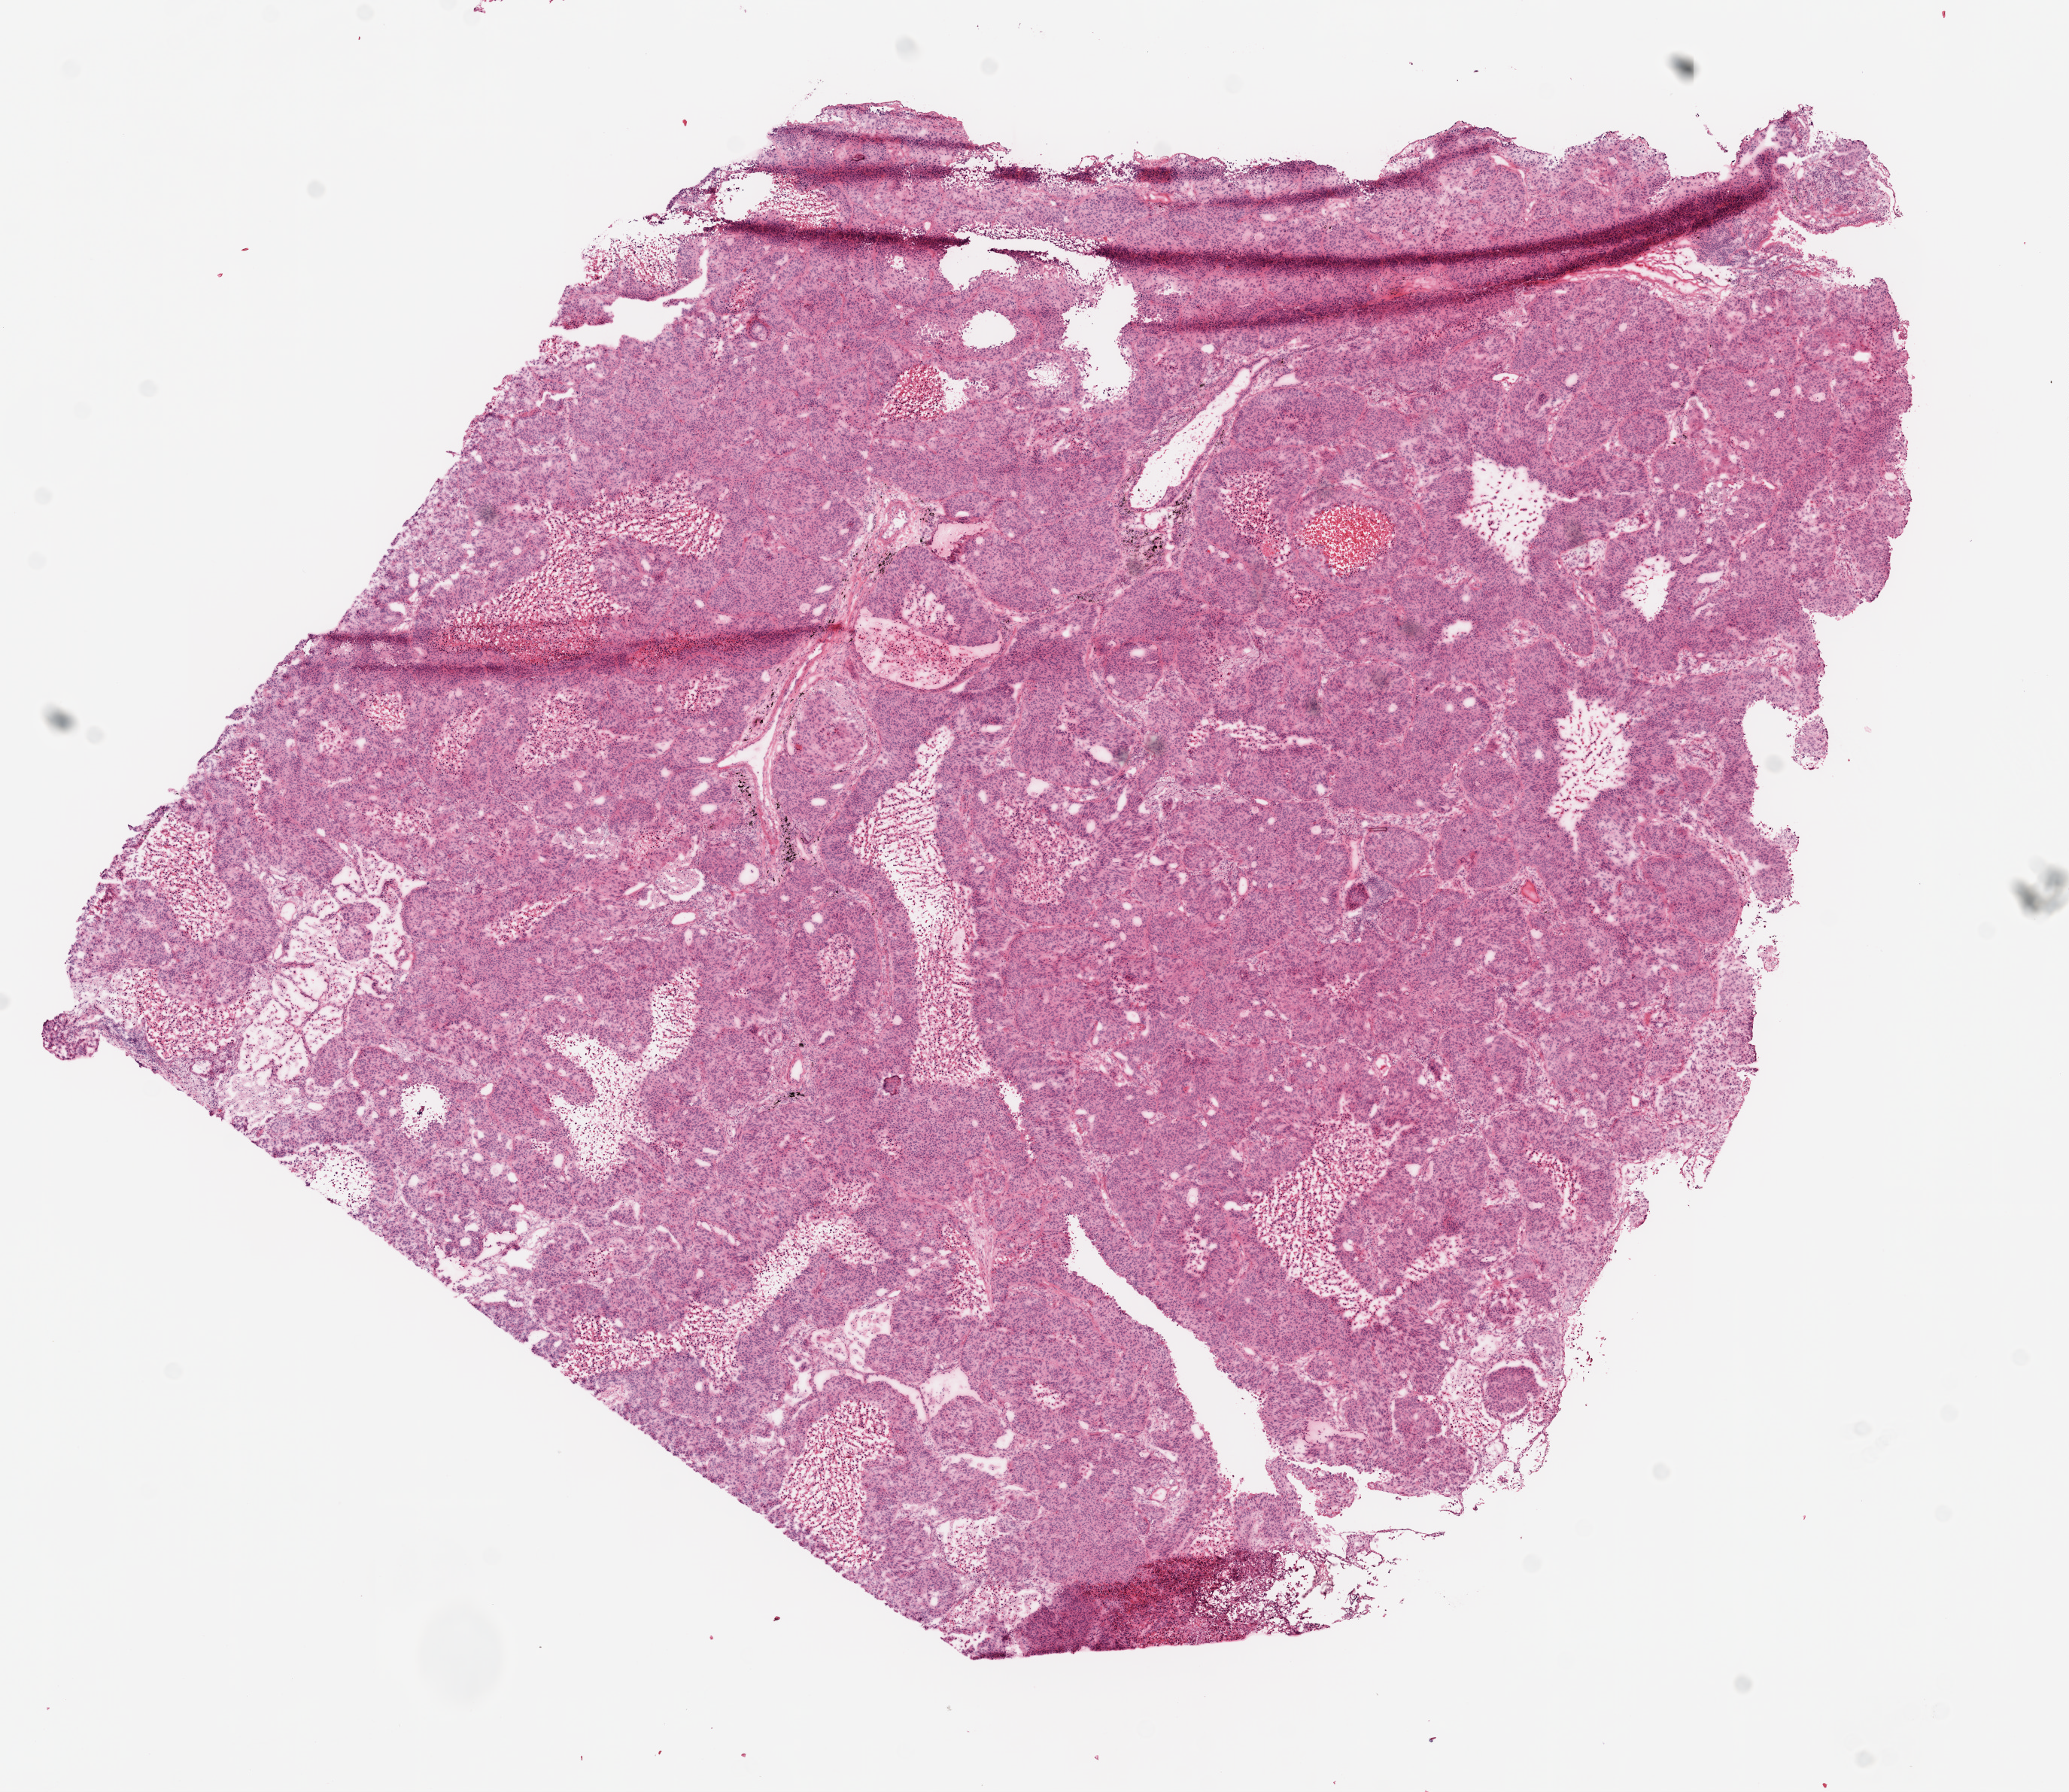
H&E-stained whole-slide image, whole scanned area (about 11.0 x 9.6 mm, from a 20x scan) shown as a low-resolution overview; frozen section from the top of the tissue portion; primary tumour sample from the lung. Male patient; age at initial diagnosis 80 years. Pathologist review of this section (percent, as recorded): tumour cells 85%, tumour nuclei 80%, normal cells 0%, stromal cells 5%, necrosis 10%.
Pathologic diagnosis: Squamous cell carcinoma, NOS (lower lobe, lung). AJCC pathologic stage: IIIA. Laterality: right.